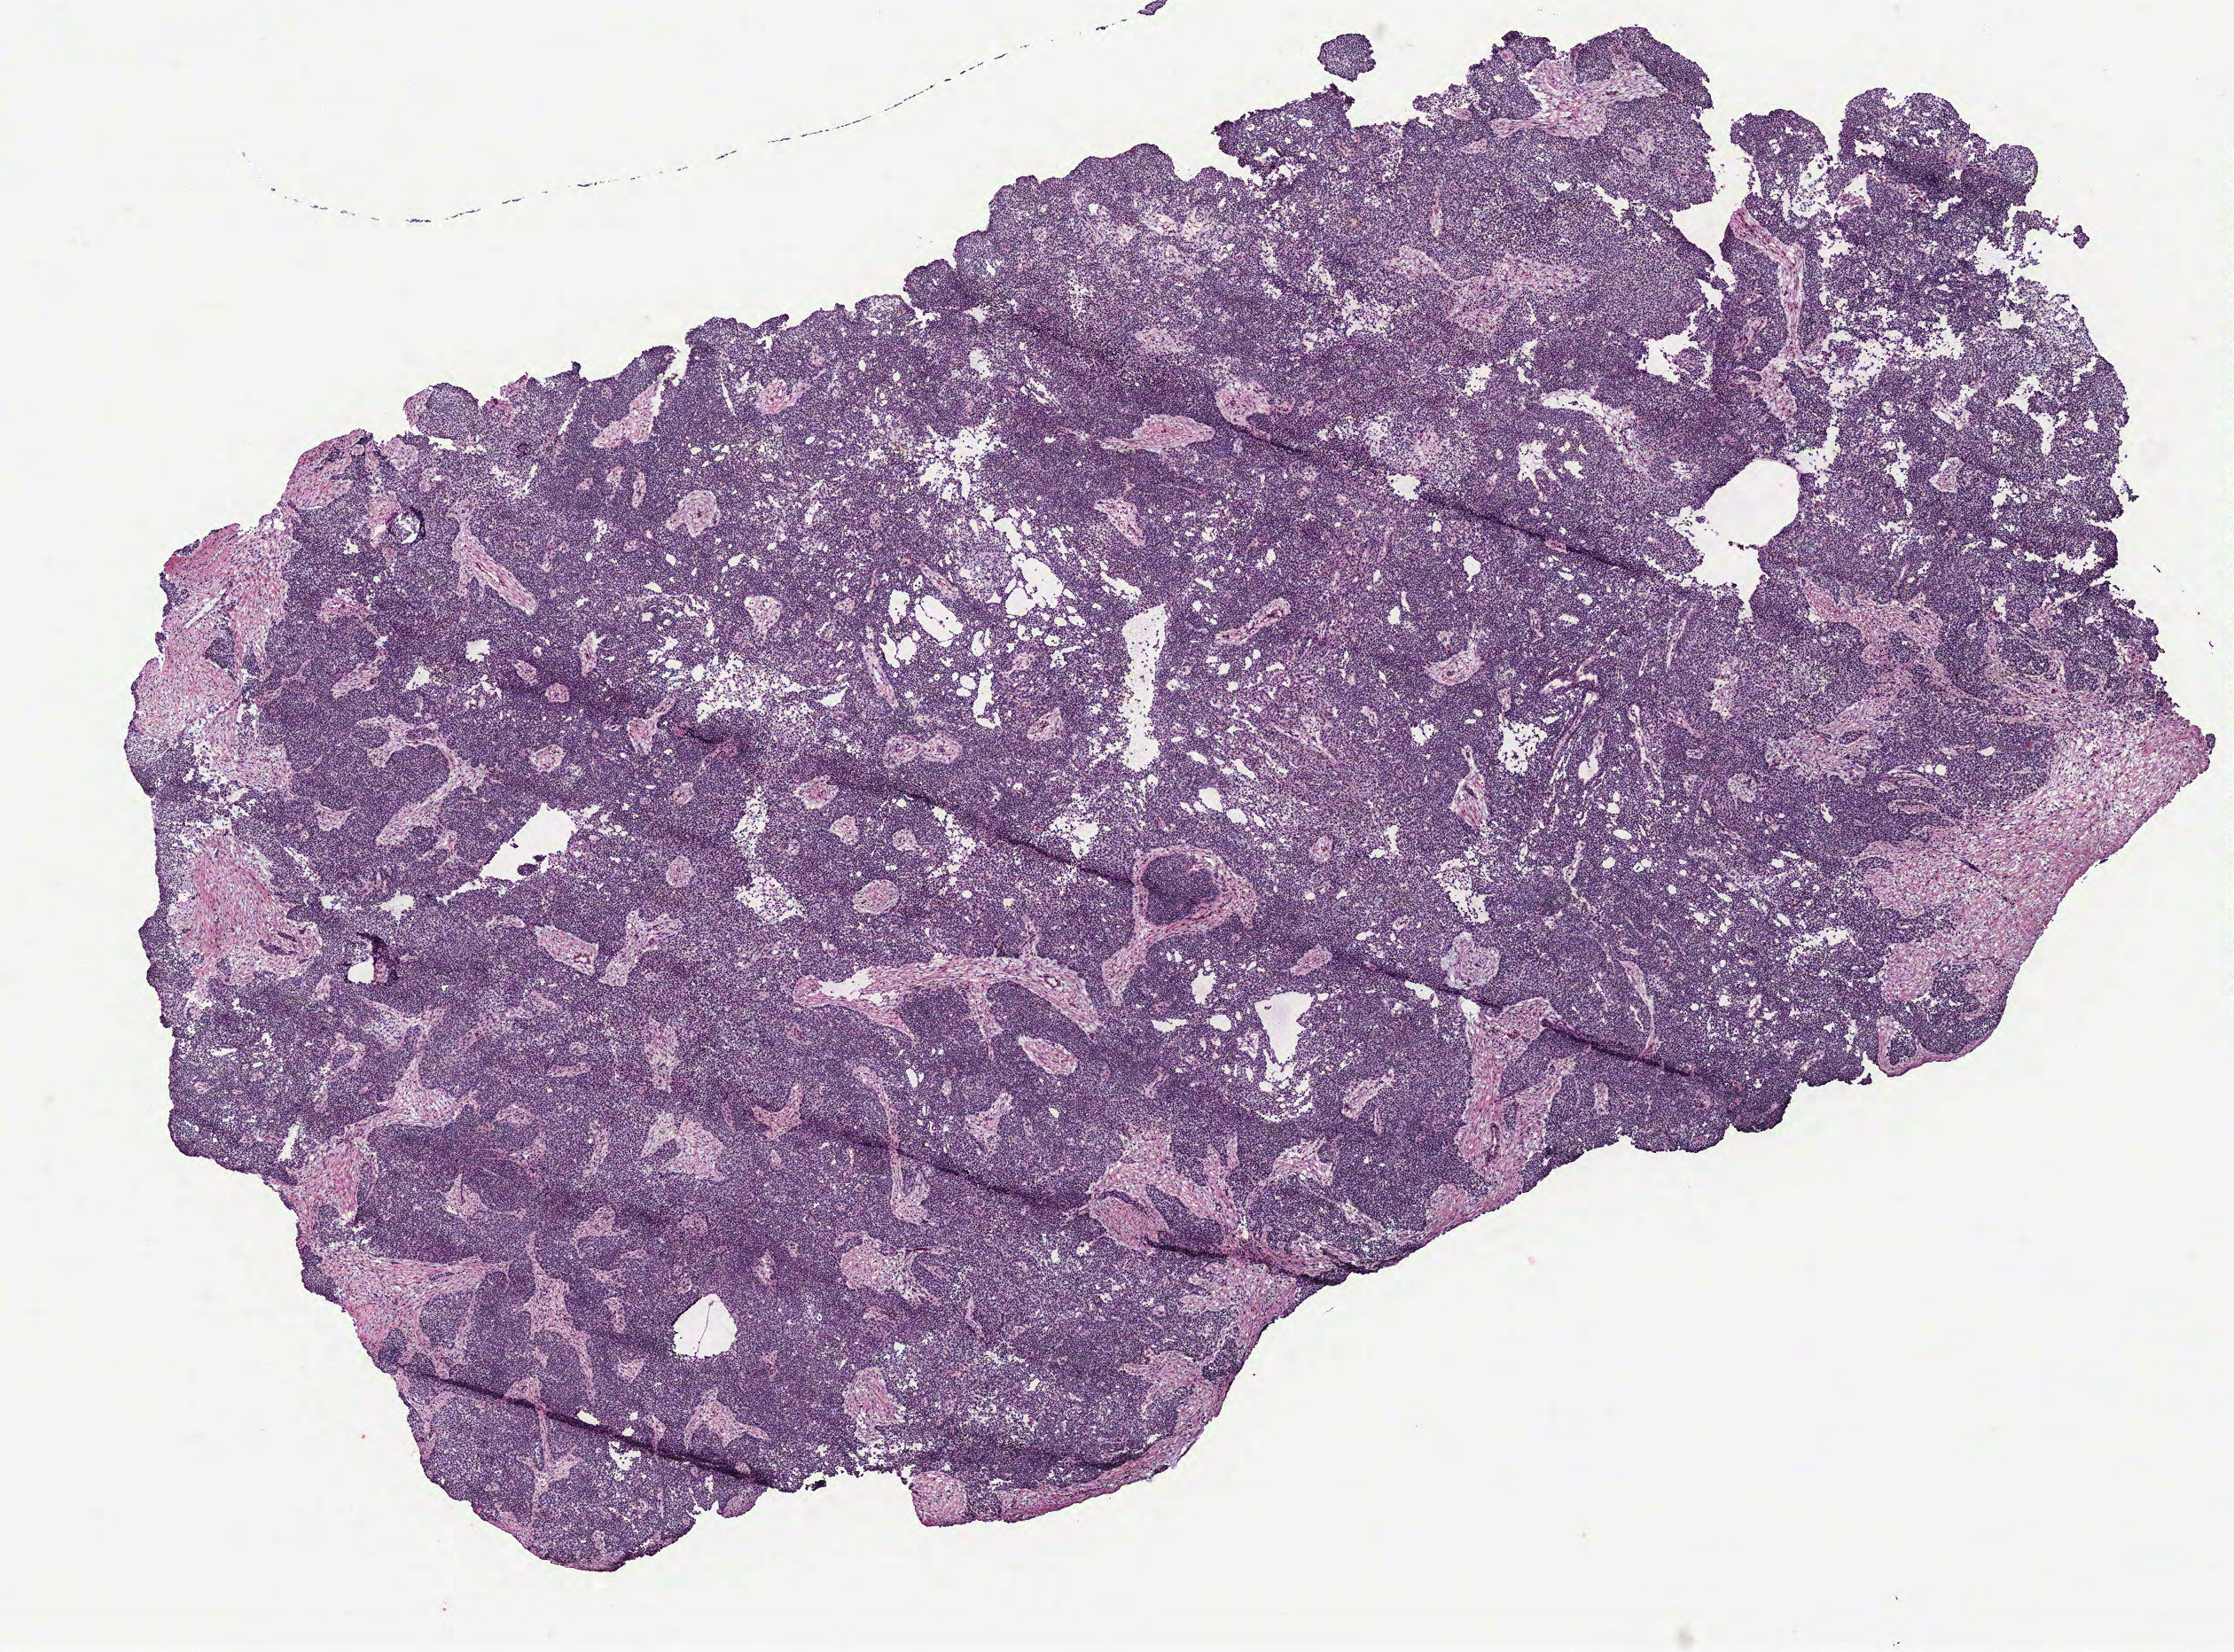
Whole-slide histology image, H&E-stained, whole scanned area (about 10.1 x 7.5 mm, acquisition: 40x scan) shown as a low-resolution overview, ovary, tumour tissue. Patient: female, age 48 years.
* primary tumour site (as recorded): ovary
* histologic diagnosis: Serous adenocarcinoma, NOS